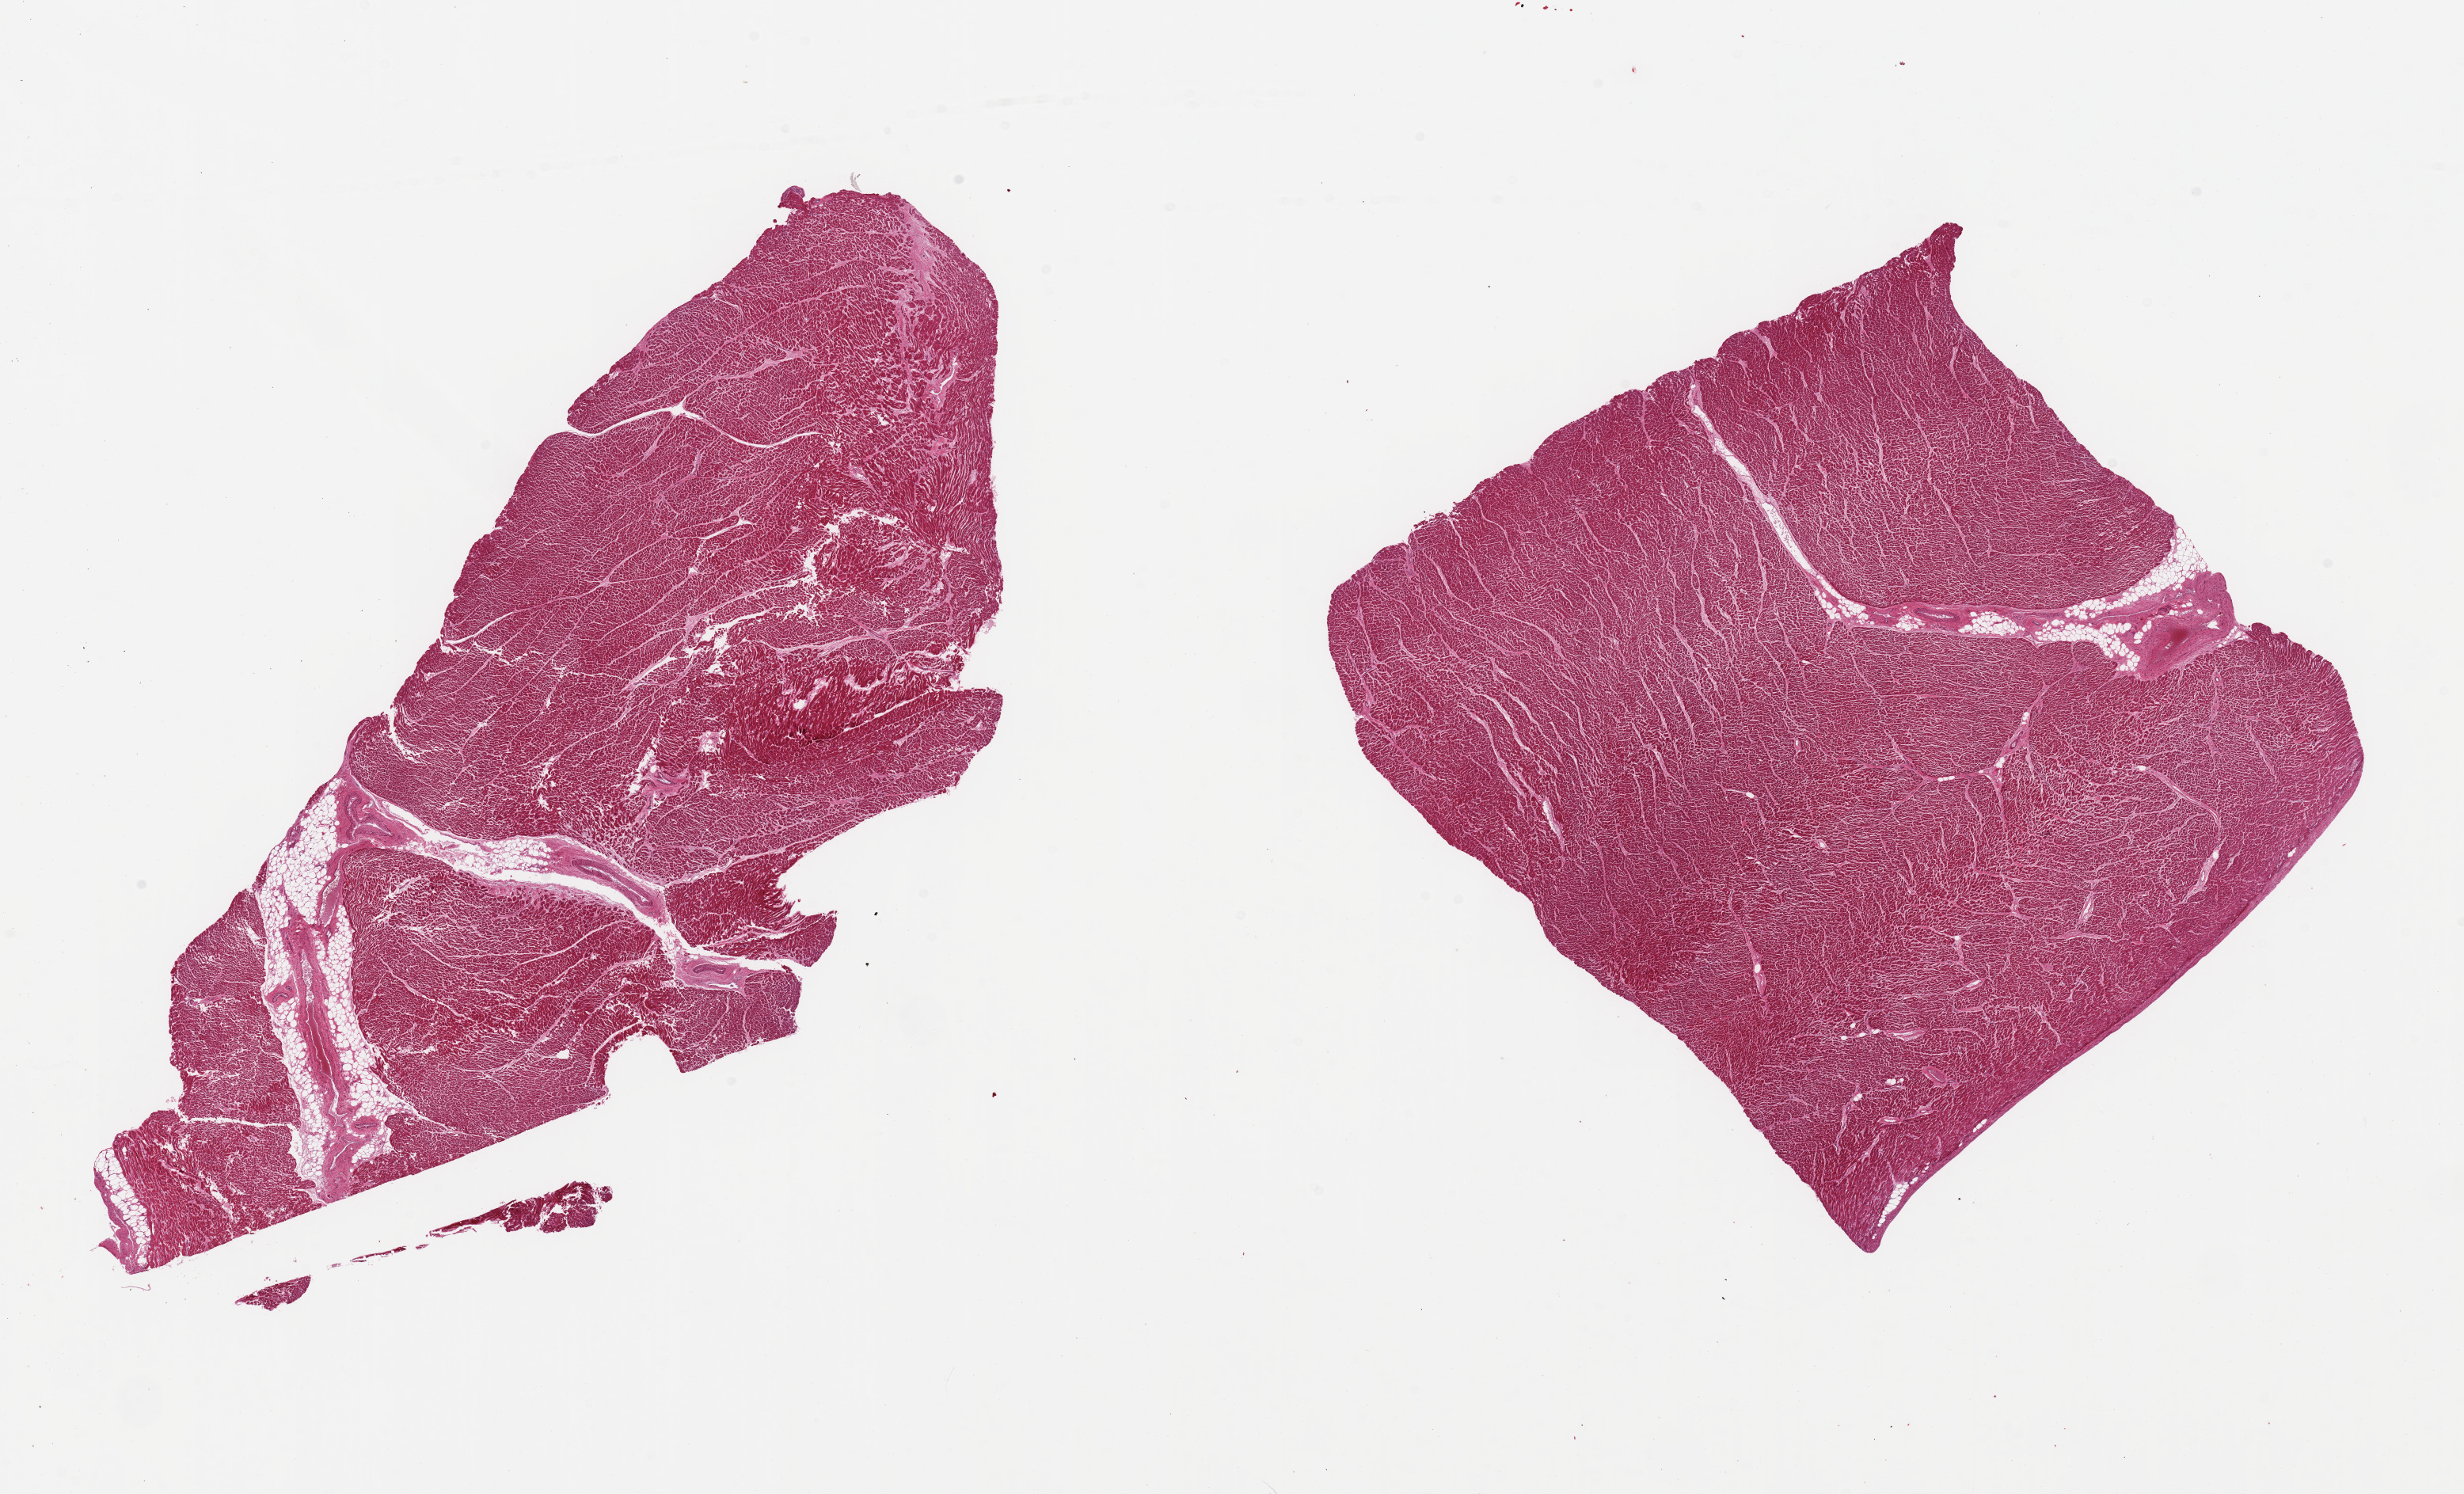
Digitized hematoxylin and eosin (H&E)-stained section — a low-resolution overview of the entire scanned area, about 24.6 x 14.9 mm; PAXgene-fixed, paraffin-embedded tissue; target tissue: heart; donor tissue sample. Male donor.
Reviewer comment on this tissue sample: 2 pieces; some interstitial fibrosis, fatty infiltration surrounding vessels.